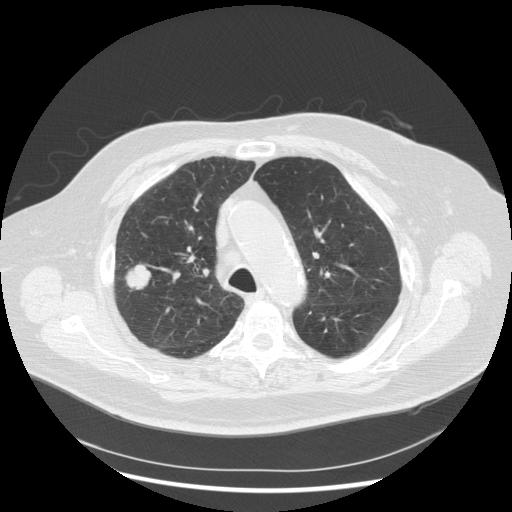
Axial slice from a low-dose chest CT screening exam, third annual screen, lung window (W 1500 / L -600 HU), 2.5 mm slice thickness, standard (soft-tissue) reconstruction kernel (STANDARD), slice 203 of 263 in the series, 512 × 512 image matrix. Male, age 72 years at enrolment. Former smoker at enrolment.
Lesion marked by an expert reader, box from (x=110, y=252) to (x=163, y=302) px. Reader record for this screening exam (exam-level; its link to the box is not recorded): non-calcified nodule or mass ≥4 mm, right upper lobe, 31 × 31 mm, poorly defined margins, soft tissue attenuation, pre-existing on the prior screen: no. Official screen result: positive, other. Lung cancer was diagnosed 70 days after this screen: squamous cell carcinoma, NOS, right upper lobe, poorly differentiated (G3), stage IIIA (AJCC 6th edition), 19 mm at pathology.